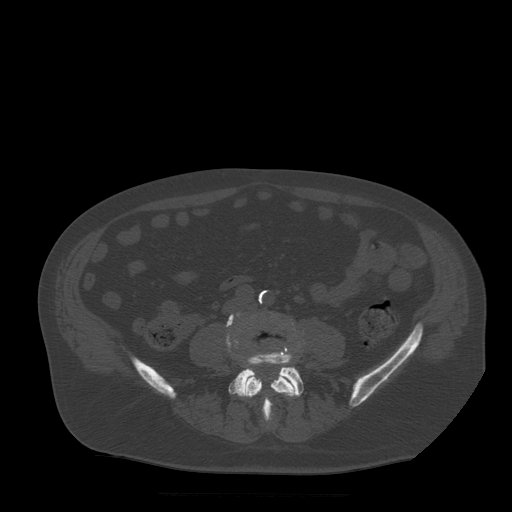
CT including the spine, one axial slice; slice 102 of 522 in the series (ordered by position); bone window (W 1800 / L 400 HU); 1.25 mm slice thickness; 512 × 512 image matrix, field of view 420 × 420 mm. Patient age 72 years. Case-level facts recorded for this patient, not image findings: primary cancer: prostate.
Annotated regions visible in this slice (semi-automatic segmentation, software-assisted and operator-edited):
- L4 vertebra: box from (x=226, y=313) to (x=297, y=422) px
- L5 vertebra: (x=227, y=322)–(x=304, y=421)